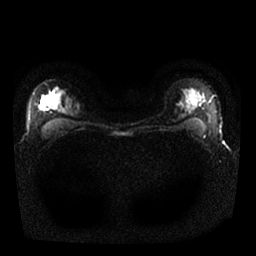
Breast MRI, one axial slice. Position 19 of 25 along the scan axis. Diffusion-weighted series; image 2 of 4 stored at this slice position (different b-values; order by instance number). 1.5 T. 256 × 256 image matrix, field of view 340 × 340 mm. Female patient.
Outlined on this slice (manually delineated by an expert):
- tumour on diffusion-weighted imaging: box from (x=40, y=101) to (x=49, y=109) px